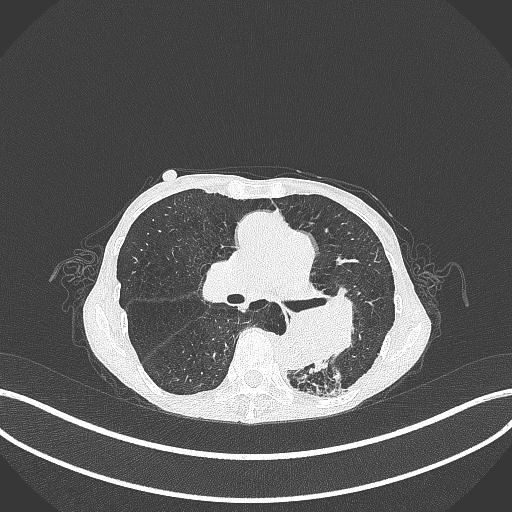
Chest CT, one axial slice. Reconstruction kernel B70f. 120 kVp. Lung window (W 1500 / L -600 HU). 1 mm slice thickness. 512 × 512 image matrix, field of view 400 × 400 mm. Patient: female, 70 years. Case-level facts recorded for this patient, not image findings: clinical TNM (as recorded): T3 N0 M0; histopathological grade: G3.
Outlined on this slice (bounding box drawn by a radiologist):
- lung tumour (recorded histology: small cell carcinoma): bounding box (x1, y1, x2, y2) in pixels: (280, 292, 369, 366)